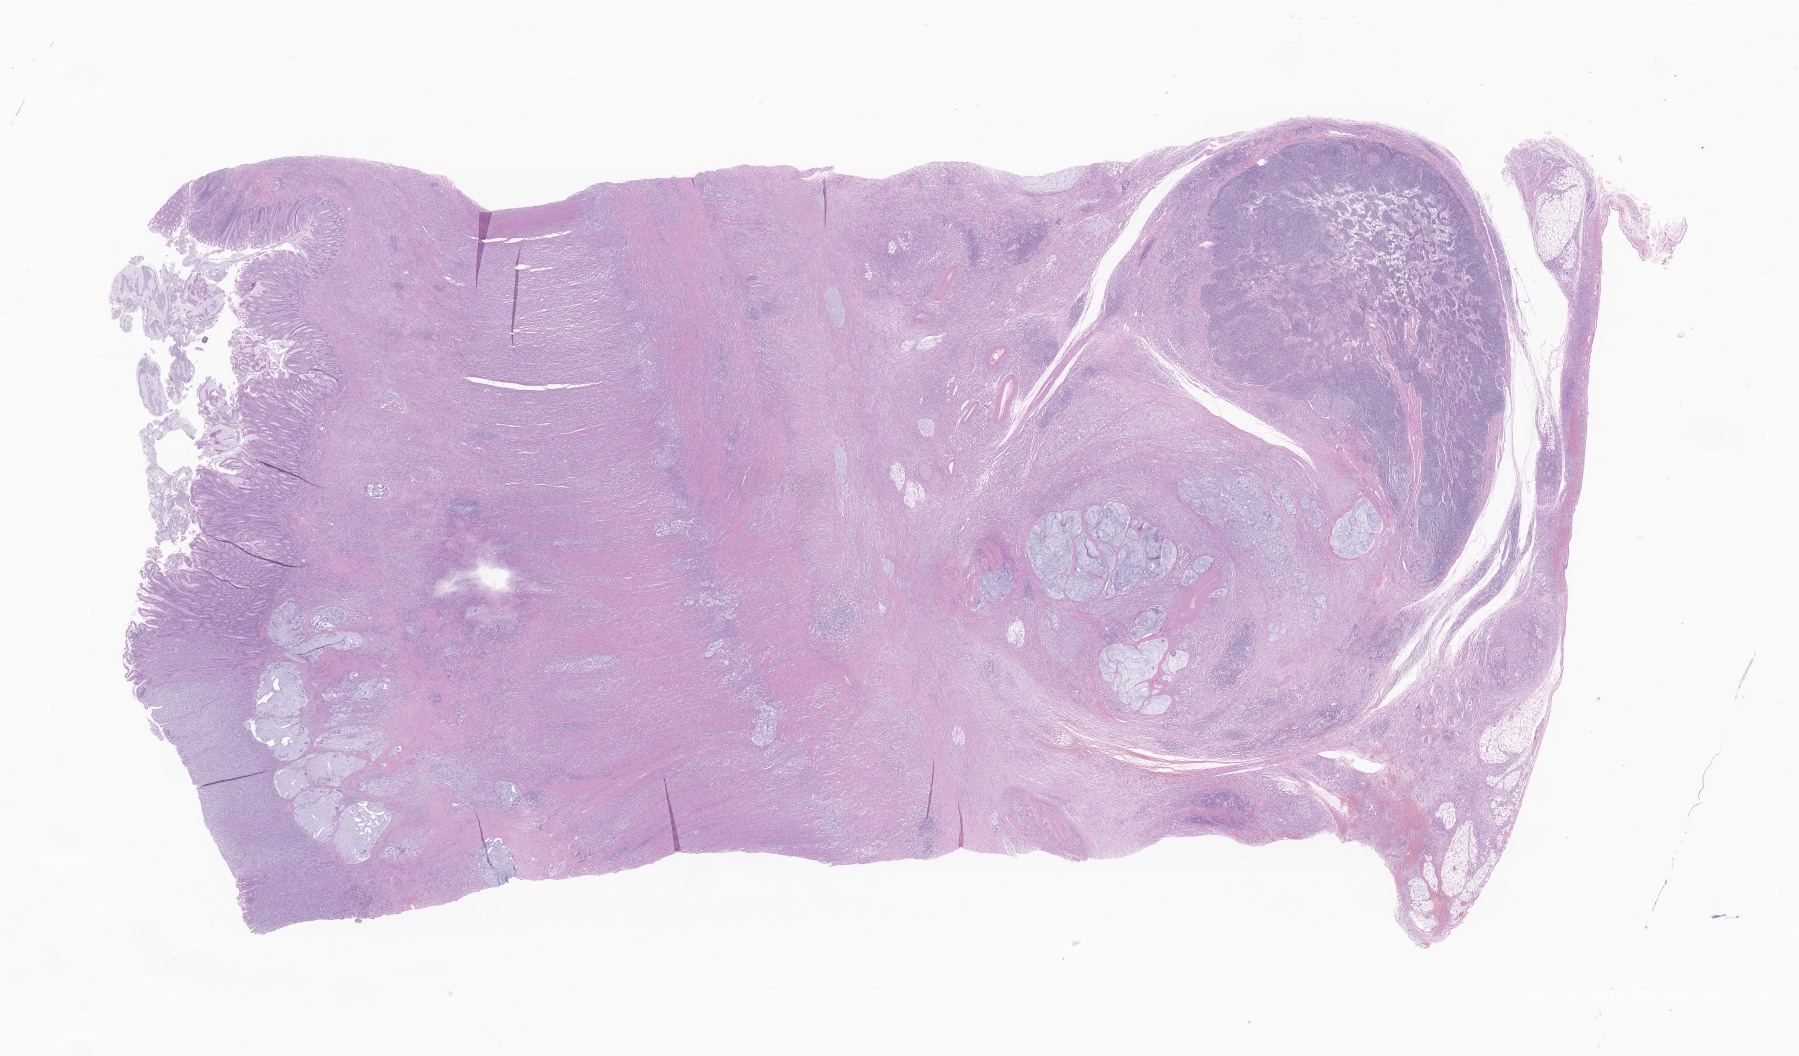
Hematoxylin and eosin (H&E) whole-slide image of tumor tissue from the colon — a low-resolution overview of the entire scanned area, about 30.3 x 17.8 mm. FFPE section. Patient male; age 191 months (15 years 11 months).
* diagnosis: Signet ring cell carcinoma